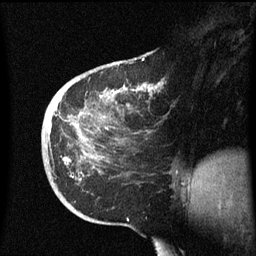
Breast MRI (dynamic contrast-enhanced), one sagittal slice. Position 23 of 60 along the scan axis. Dynamic contrast-enhanced series, image 2 of 3 at this slice position (ordered by acquisition). 1.5 T. TE 4.2 ms, TR 8.4 ms. 2.3 mm slice thickness. 256 × 256 image matrix, field of view 200 × 200 mm. Patient: female, 38 years. From the clinical record (not read from this slice): setting: breast cancer imaged before/during neoadjuvant chemotherapy; receptor status: HER2-positive.
Structures marked on this image (semi-automatic segmentation, software-assisted and operator-edited):
- analysis volume of interest (the breast-tissue region the enhancement analysis was run in; not a lesion): box from (x=42, y=78) to (x=172, y=213) px
- tumour enhancement mask (voxels above the 70 % enhancement threshold inside the analysis volume of interest): (x=113, y=84)–(x=160, y=93)